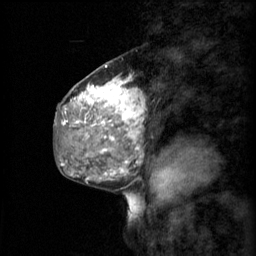
Breast MRI (dynamic contrast-enhanced), one sagittal slice; slice 29 of 60 in the series (ordered by position); 3 images stored at this slice position (order not interpretable as contrast timing); 1.5 T; TE 4.2 ms, TR 11 ms; 2 mm slice thickness; 256 × 256 image matrix, field of view 200 × 200 mm. Female patient, age 48 years.
Outlined on this slice (semi-automatic segmentation, software-assisted and operator-edited):
- analysis volume of interest (the breast-tissue region the enhancement analysis was run in; not a lesion): box from (x=69, y=74) to (x=146, y=147) px
- tumour enhancement mask (voxels above the 70 % enhancement threshold inside the analysis volume of interest): (x=74, y=78)–(x=145, y=145)